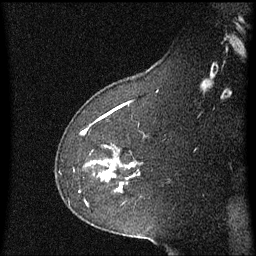
Breast MRI (dynamic contrast-enhanced), one sagittal slice. Slice 41 of 60 in the series (ordered by position). Dynamic contrast-enhanced series, image 2 of 3 at this slice position (ordered by acquisition). 1.5 T. TE 4.2 ms, TR 8.4 ms. 2.2 mm slice thickness. 256 × 256 image matrix, field of view 200 × 200 mm. Female patient, age 60 years. From the clinical record (not read from this slice): setting: breast cancer imaged before/during neoadjuvant chemotherapy; receptor status: triple-negative.
Structures marked on this image (semi-automatic segmentation, software-assisted and operator-edited):
- analysis volume of interest (the breast-tissue region the enhancement analysis was run in; not a lesion): bounding box <96,146,140,193> (left, top, right, bottom; pixels)
- tumour enhancement mask (voxels above the 70 % enhancement threshold inside the analysis volume of interest): <96,162,131,189>